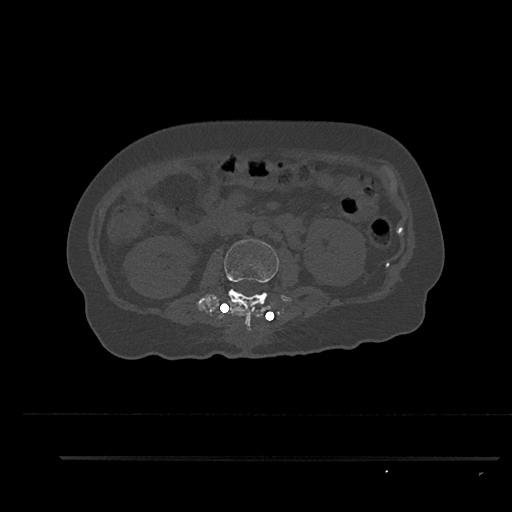
CT including the spine, one axial slice. Position 146 of 797 along the scan axis. Reconstruction kernel Br40s/3. Bone window (W 1800 / L 400 HU). 0.5 mm slice thickness. 512 × 512 image matrix, field of view 408 × 408 mm. Patient: female, 44 years. Case-level facts recorded for this patient, not image findings: primary cancer: renal; vertebrae with lytic lesions (as recorded): L1.
Structures marked on this image (semi-automatically segmented with operator editing):
- L2 vertebra: box from (x=196, y=239) to (x=279, y=329) px